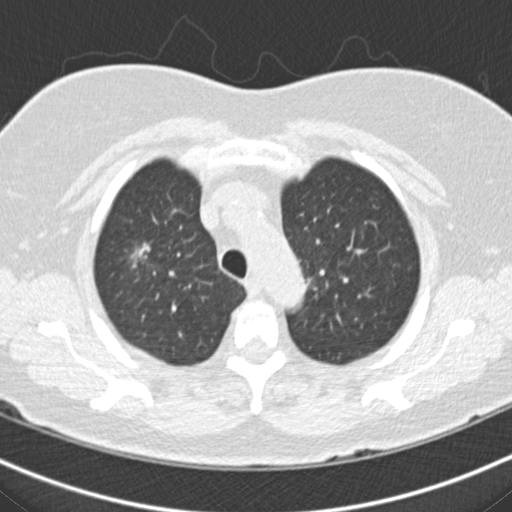
Low-dose screening chest CT, one axial slice. Slice 136 of 160 in the series (ordered by position). Reconstruction kernel B30f. 120 kVp. Lung window (W 1500 / L -600 HU). 2 mm slice thickness. 512 × 512 image matrix, field of view 316 × 316 mm.
Structures marked on this image (expert manual segmentation):
- lesion 3 (nodule, upper lobe of right lung): bounding box [x1, y1, x2, y2] px = [133, 245, 148, 259]